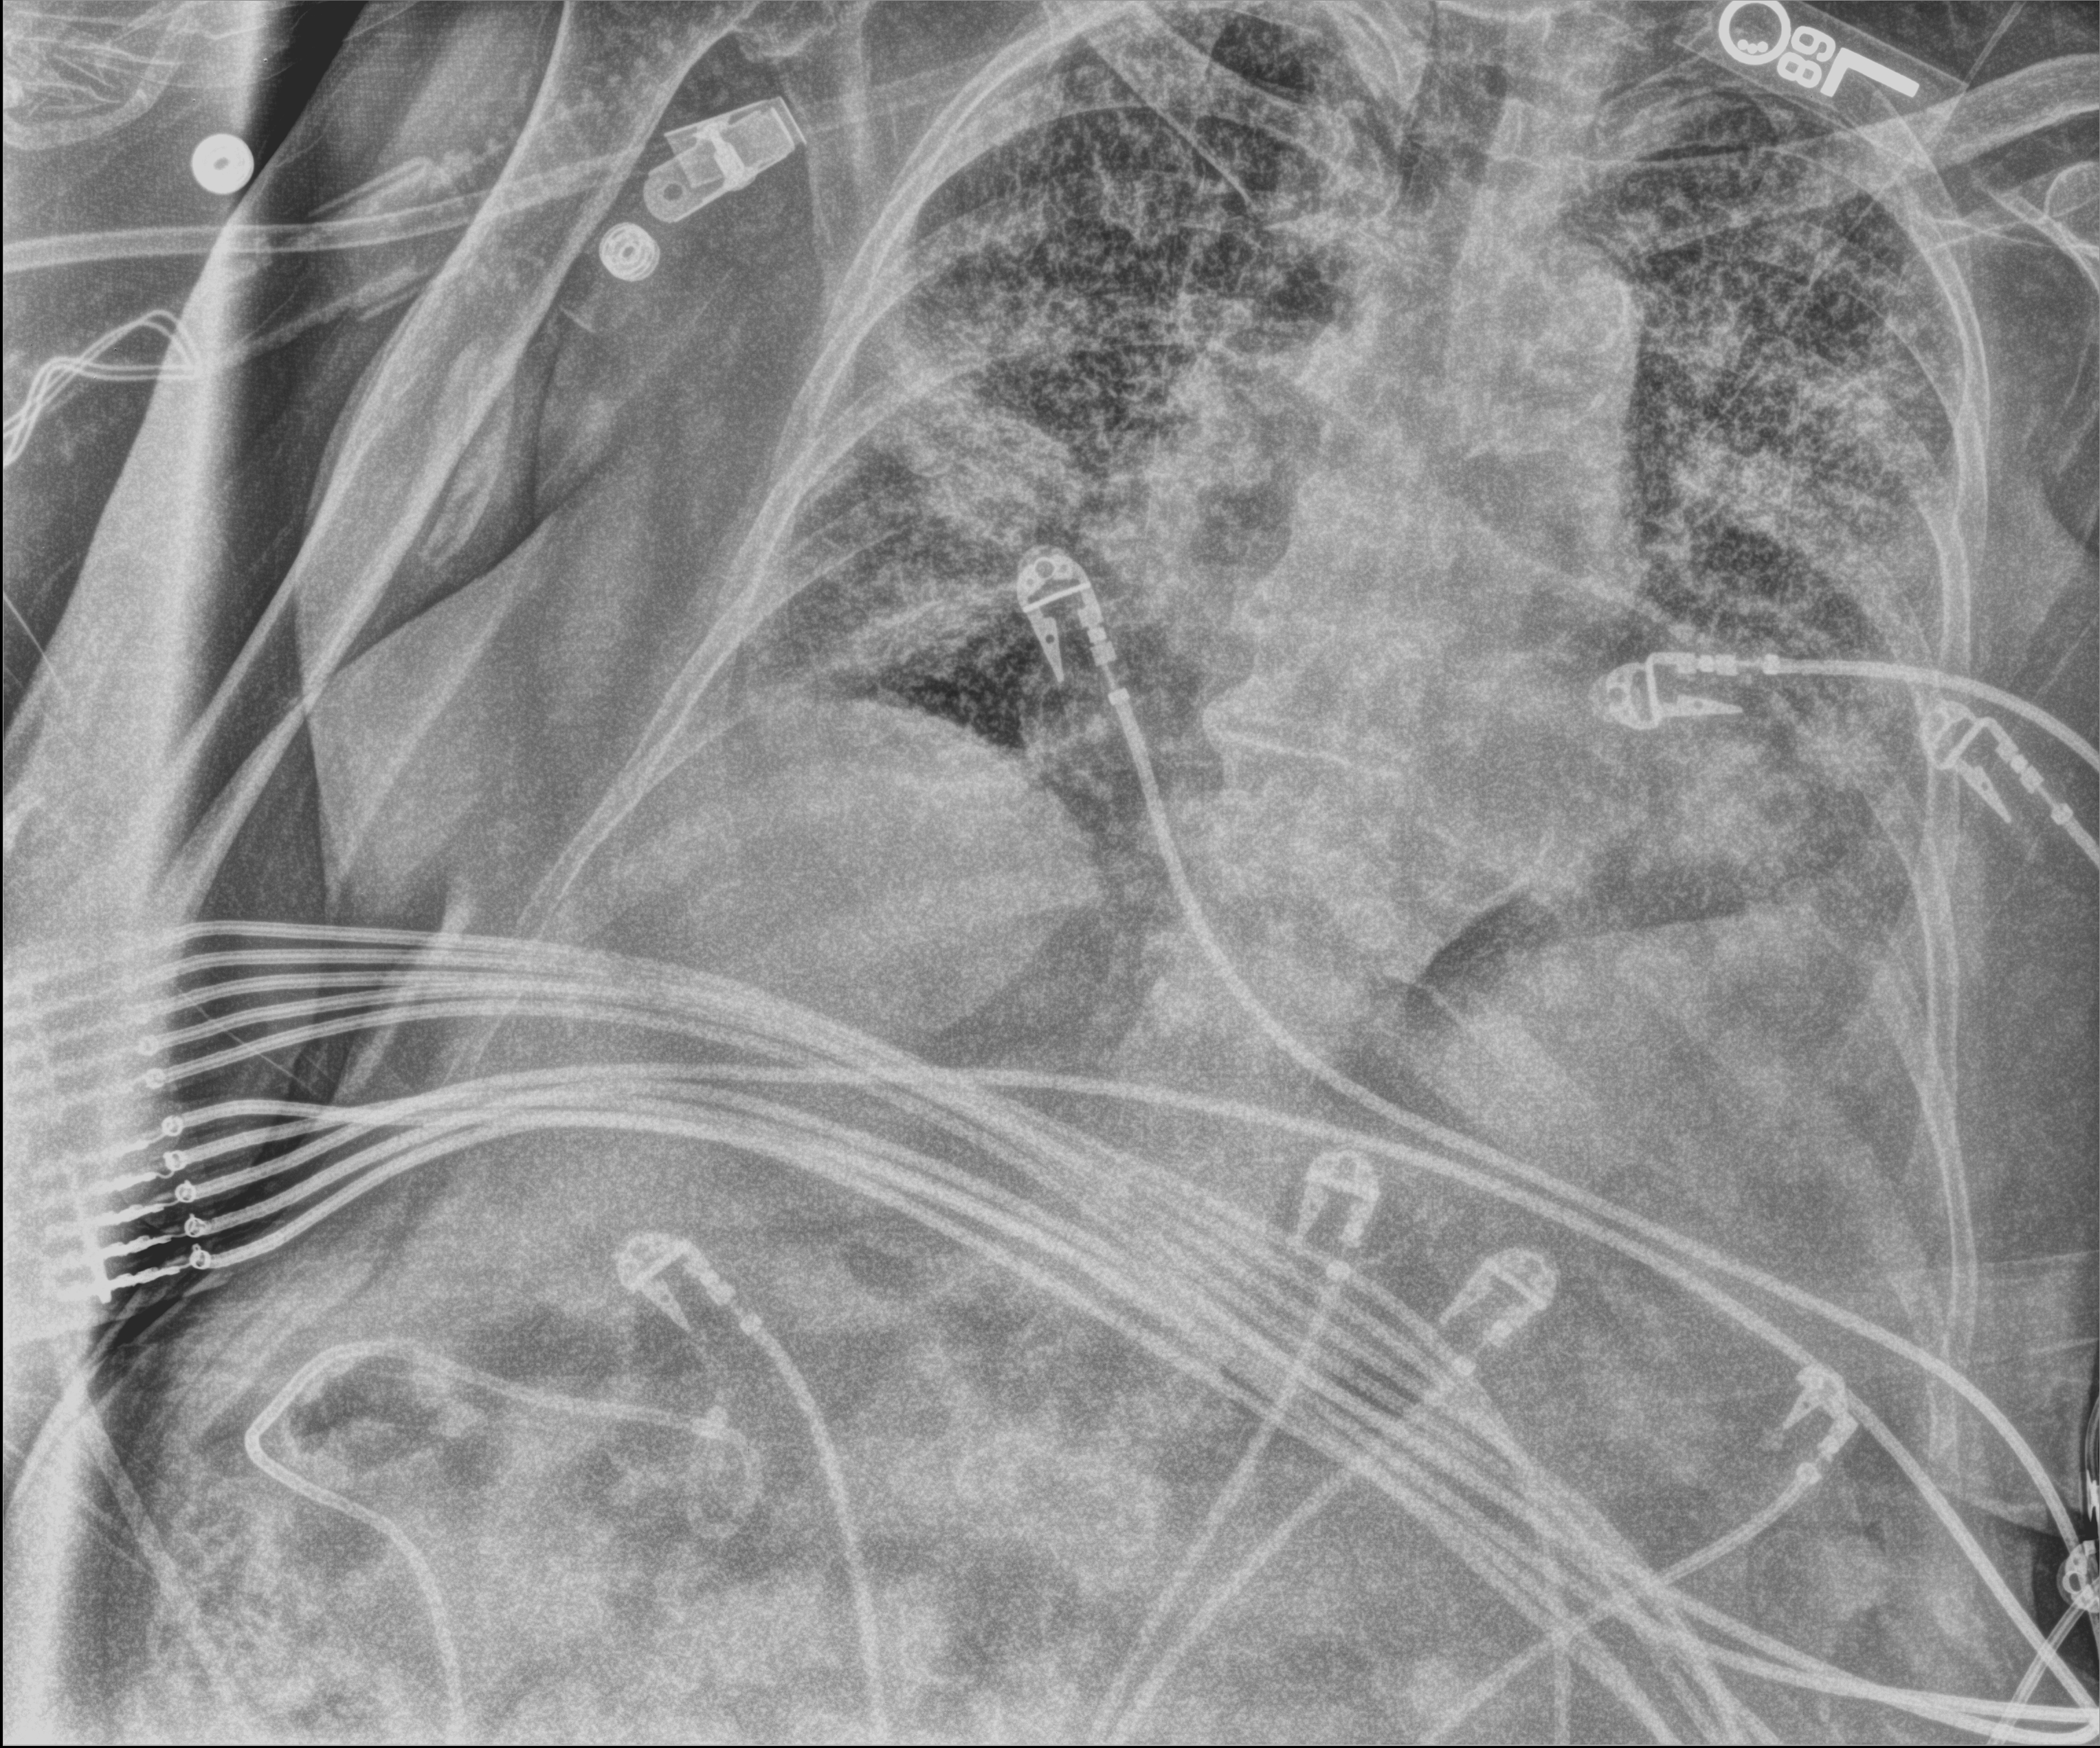
Chest X-ray (portable), anteroposterior (AP) projection. Female patient hospitalised with COVID-19, age 75–90 years.
Admission-level facts for this patient (not findings on this image; timing relative to this image not recorded): admitted to intensive care during this hospital stay: no; mechanically ventilated during this hospital stay: no.